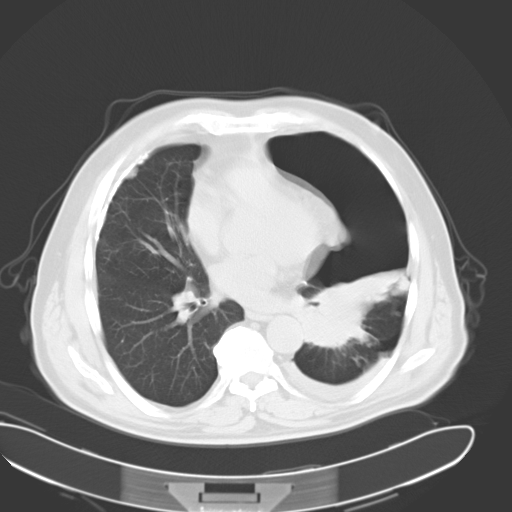
Chest CT, one axial slice. Slice 17 of 34 in the series (ordered by position). 120 kVp. Lung window (W 1500 / L -600 HU). 10 mm slice thickness. 512 × 512 image matrix. Male patient, age 62 years. From the clinical record (not read from this slice): clinical TNM (as recorded): T3 N0 M1.
Outlined on this slice (rectangle marked by the reading radiologist):
- lung tumour (recorded histology: adenocarcinoma): bounding box (x1, y1, x2, y2) in pixels: (296, 290, 365, 350)
- lung tumour (recorded histology: adenocarcinoma): (297, 287, 377, 359)